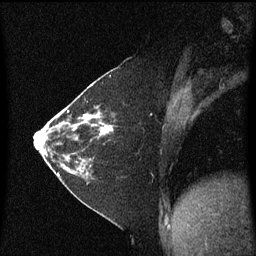
Breast MRI (dynamic contrast-enhanced), one sagittal slice. Slice 27 of 60 in the series (ordered by position). Dynamic contrast-enhanced series, image 2 of 3 at this slice position (ordered by acquisition). 1.5 T. TE 4.2 ms, TR 8.4 ms. 2 mm slice thickness. 256 × 256 image matrix, field of view 200 × 200 mm. Female patient, age 36 years. From the clinical record (not read from this slice): setting: breast cancer imaged before/during neoadjuvant chemotherapy; receptor status: HR-positive, HER2-negative.
Structures marked on this image (semi-automatic segmentation, software-assisted and operator-edited):
- analysis volume of interest (the breast-tissue region the enhancement analysis was run in; not a lesion): bounding box (x1, y1, x2, y2) in pixels: (66, 102, 115, 179)
- tumour enhancement mask (voxels above the 70 % enhancement threshold inside the analysis volume of interest): (83, 112, 113, 137)